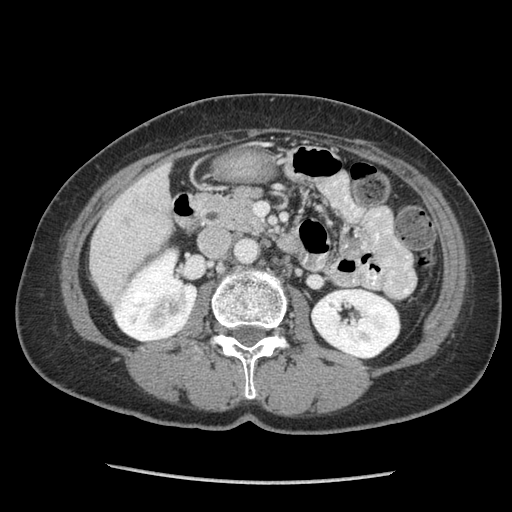
Contrast-enhanced abdominal CT (liver protocol), one axial slice. Position 26 of 105 along the scan axis. Reconstruction kernel STANDARD. 140 kVp. Soft-tissue window (W 400 / L 40 HU). 2.5 mm slice thickness. 512 × 512 image matrix, field of view 340 × 340 mm. Case-level facts recorded for this patient, not image findings: diagnosis: hepatocellular carcinoma (patient treated with transarterial chemoembolisation; whether this scan precedes or follows treatment is not stated here); TNM stage (as recorded): Stage-I; Child-Pugh class: A; tumour differentiation: moderately differentiated; tumour nodularity: uninodular.
Annotated regions visible in this slice (semi-automatically segmented with operator editing):
- liver parenchyma outside the tumour (the mass and vessels are separate outlines, so this box may not span the whole liver): box from (x=90, y=162) to (x=172, y=301) px
- liver vessels: (x=106, y=180)–(x=148, y=239)